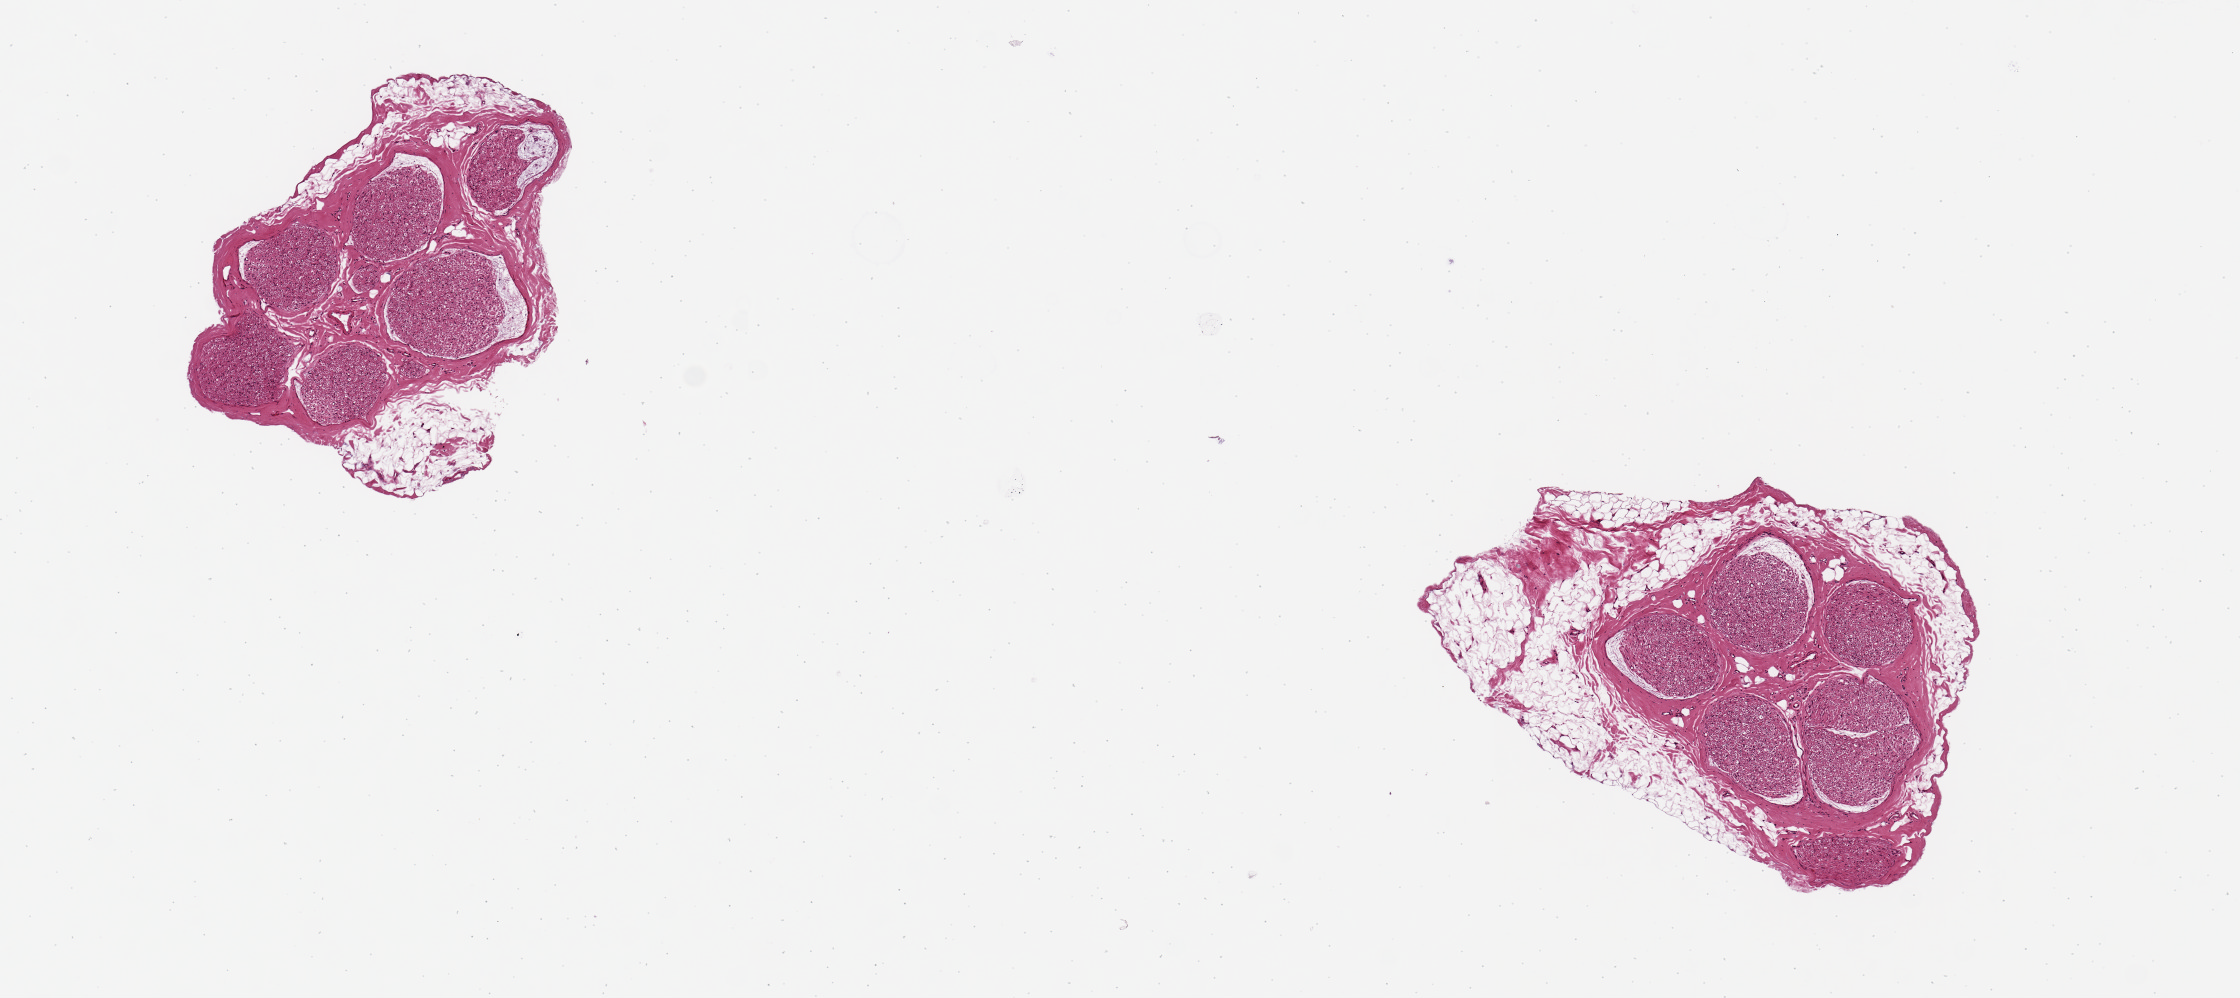
Hematoxylin and eosin (H&E) whole-slide image, low-resolution overview of the scanned area, about 8.9 x 3.9 mm. PAXgene-fixed paraffin-embedded (PFPE) section. Sampled site (target tissue): tibial nerve. Donor tissue sample. Female donor.
Pathologist's review note for this sample: 2 pieces 2x1 & 2x1 mm; ~30-40 % peripheral adipose.